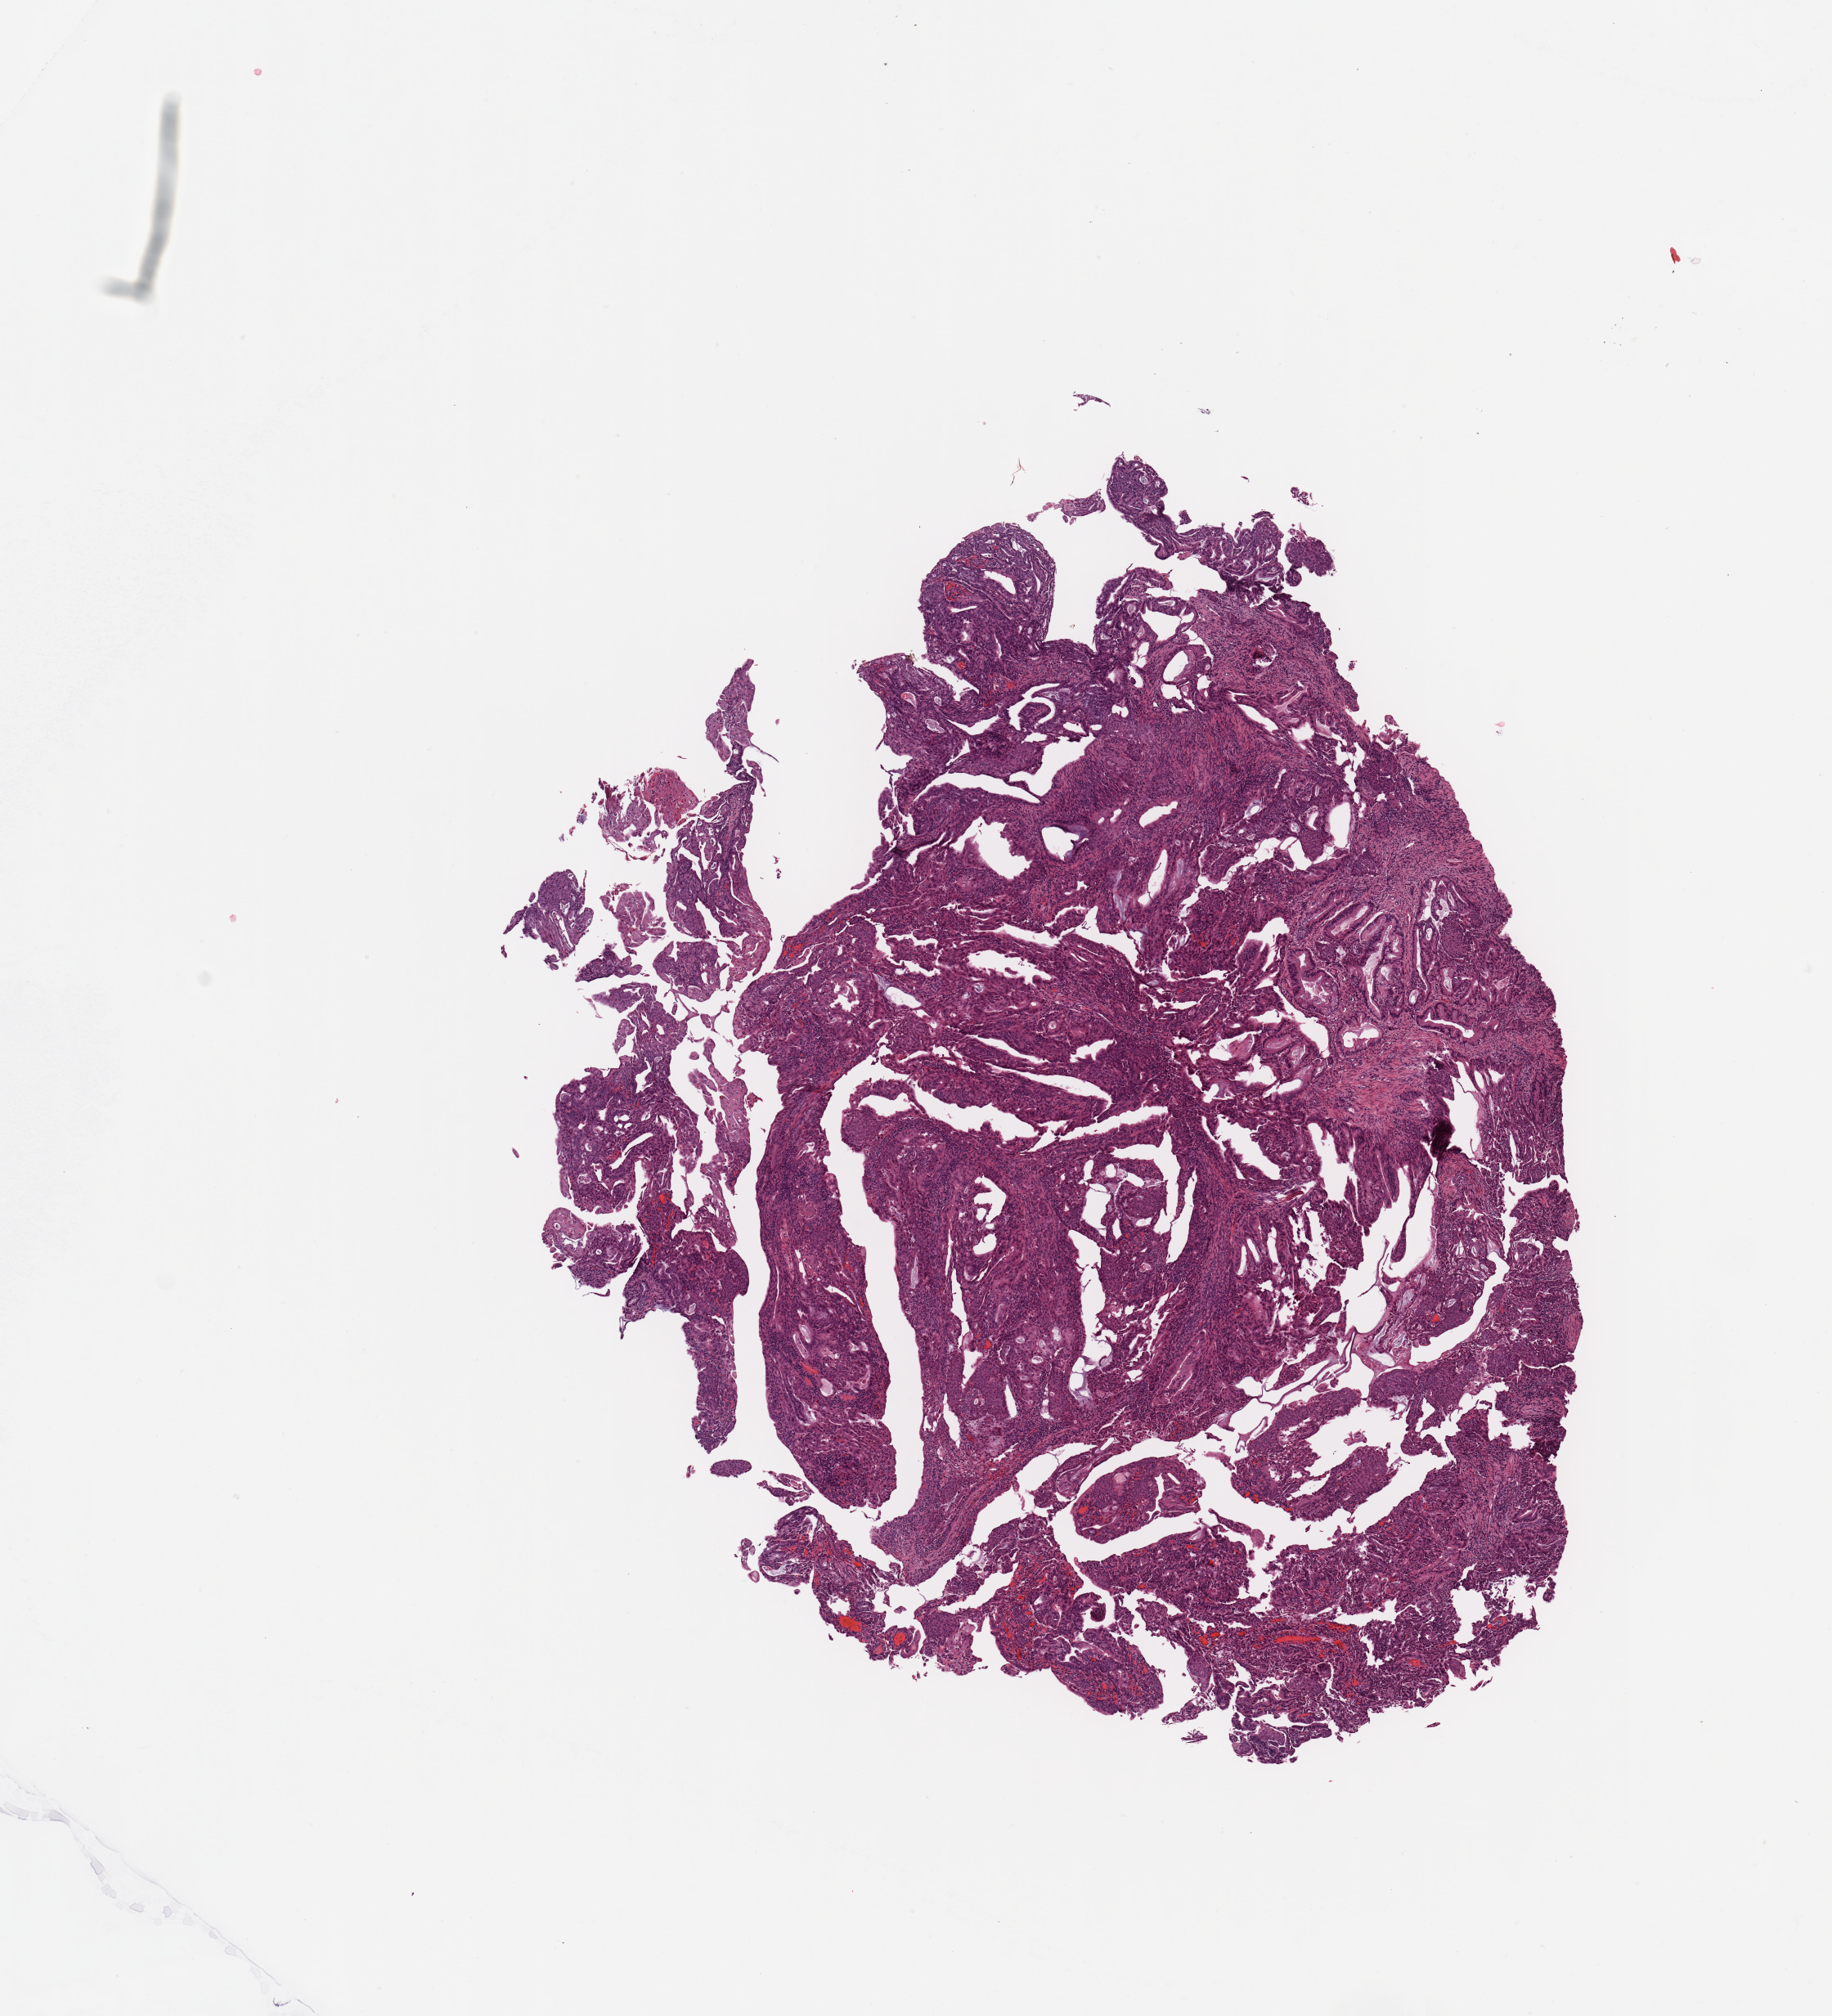
Digitized H&E-stained tissue section (whole slide) — whole scanned area (about 8.9 x 9.7 mm, from a 20x scan) shown as a low-resolution overview. Tumour tissue sample, sampled site: uterus. 54-year-old female patient. Histologic grade: G2 (moderately differentiated). Pathologist review of this section (percent, as recorded): tumour nuclei 90%, necrosis 0%.
• AJCC pathologic stage: IIIB
• diagnosis: Endometrioid adenocarcinoma, NOS